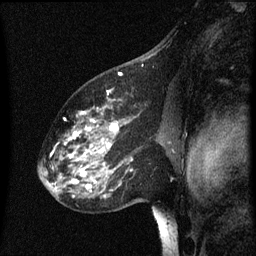
Breast MRI (dynamic contrast-enhanced), one sagittal slice. Position 40 of 60 along the scan axis. Dynamic contrast-enhanced series, image 2 of 3 at this slice position (ordered by acquisition). 1.5 T. TE 4.2 ms, TR 8 ms. 256 × 256 image matrix, field of view 200 × 200 mm. Patient: female, 60 years.
Structures marked on this image (semi-automatically segmented with operator editing):
- analysis volume of interest (the breast-tissue region the enhancement analysis was run in; not a lesion): box from (x=49, y=100) to (x=152, y=197) px
- tumour enhancement mask (voxels above the 70 % enhancement threshold inside the analysis volume of interest): (x=56, y=112)–(x=134, y=197)